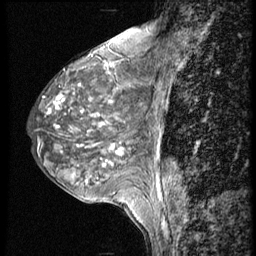
Breast MRI (dynamic contrast-enhanced), one sagittal slice; slice 21 of 56 in the series (ordered by position); 4 images stored at this slice position (order not interpretable as contrast timing); 1.5 T; TE 4.2 ms, TR 9 ms; 2.5 mm slice thickness; 256 × 256 image matrix. Patient: female, 50 years. Case-level facts recorded for this patient, not image findings: setting: breast cancer imaged before/during neoadjuvant chemotherapy; receptor status: triple-negative.
Structures marked on this image (semi-automatic segmentation, software-assisted and operator-edited):
- analysis volume of interest (the breast-tissue region the enhancement analysis was run in; not a lesion): bounding box (x1, y1, x2, y2) in pixels: (27, 46, 148, 188)
- tumour enhancement mask (voxels above the 140 % enhancement threshold inside the analysis volume of interest): (47, 65, 122, 166)